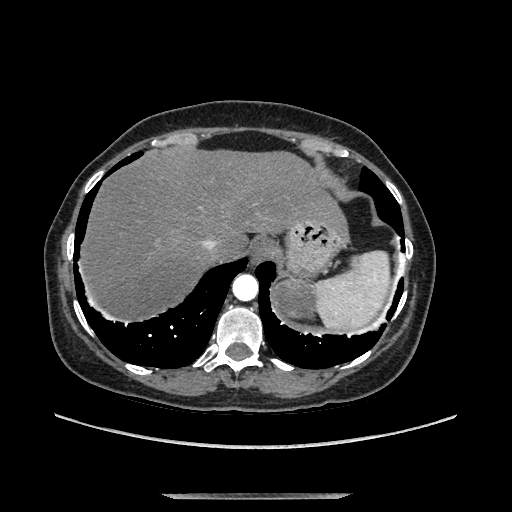
Contrast-enhanced abdominal CT, one axial slice. Slice 117 of 169 in the series (ordered by position). Soft-tissue window (W 400 / L 40 HU). 512 × 512 image matrix, field of view 400 × 400 mm. Female patient. From the clinical record (not read from this slice): diagnosis: adrenocortical carcinoma; tumour side: left adrenal; tumour size at pathology: 9 cm; Ki-67 index: 2 %; stage (as recorded): 3.
Annotated regions visible in this slice (semi-automatically segmented with operator editing):
- mass: bounding box (x1, y1, x2, y2) in pixels: (277, 279, 314, 315)